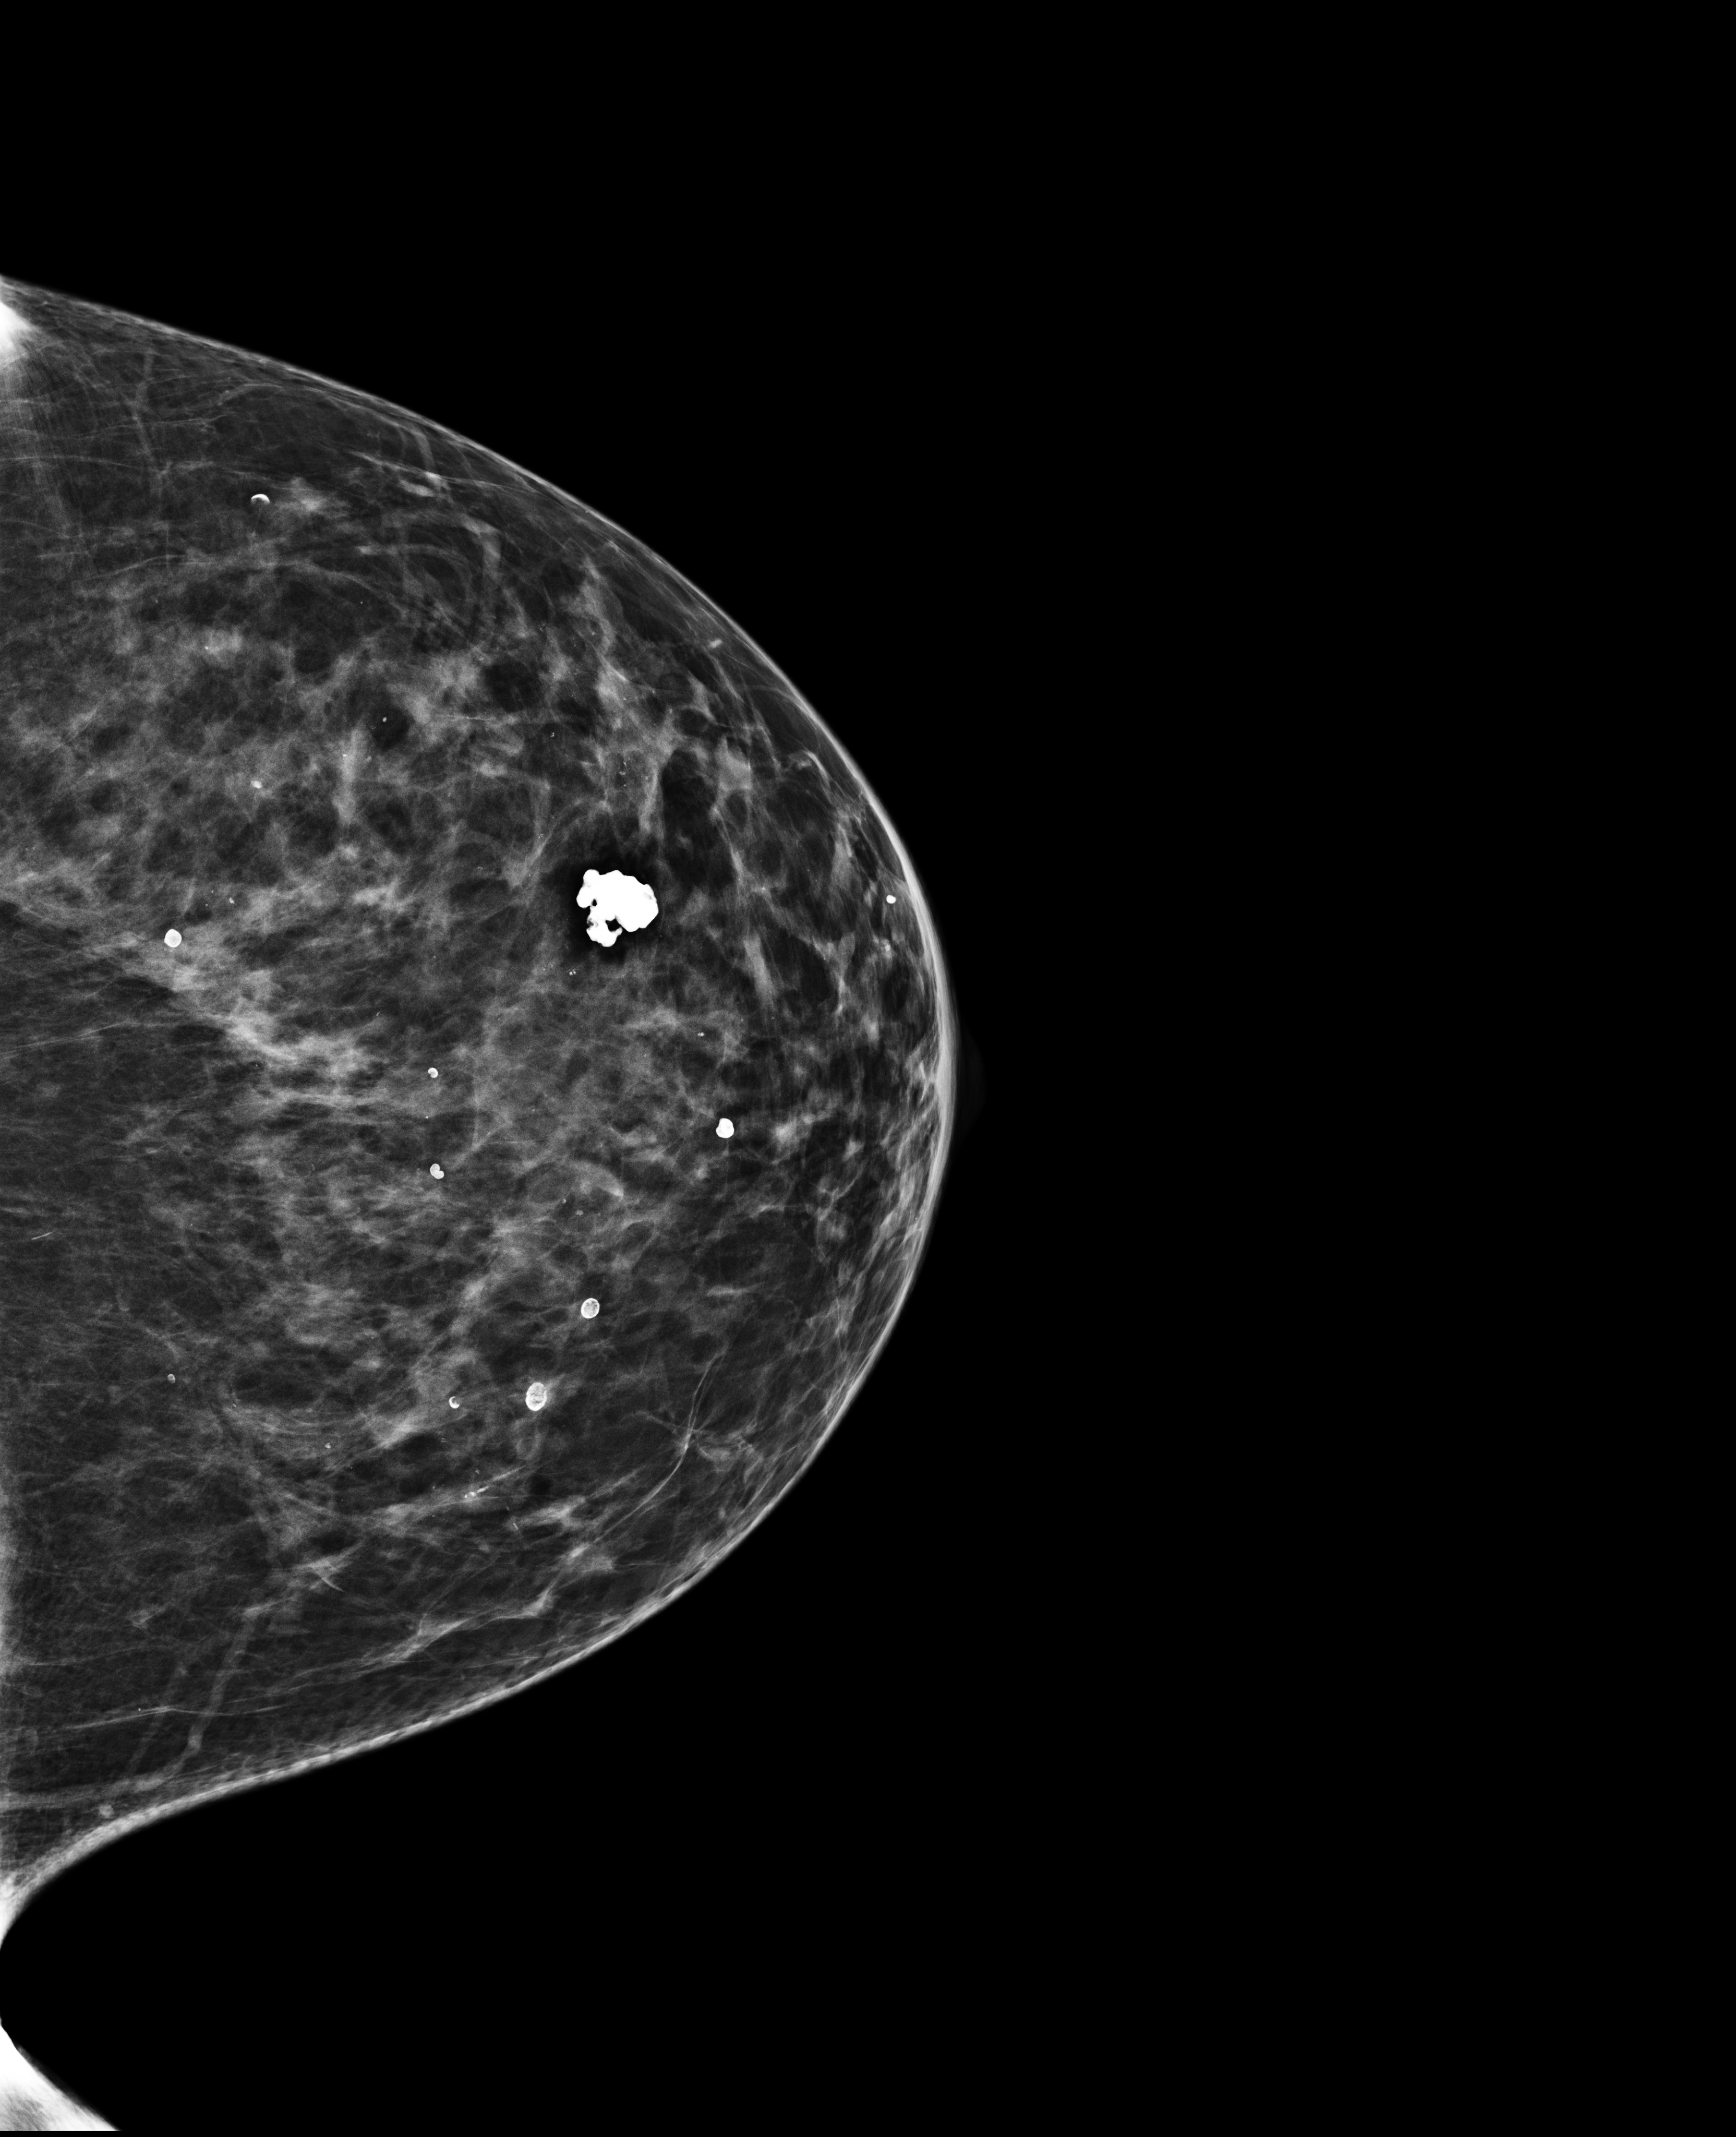
Annual screening mammography examination; compressed breast thickness 70 mm; system: Selenia Dimensions. Patient aged 66 years (female).
Image type: full-field digital mammogram. Breast: left. Projection: CC view.